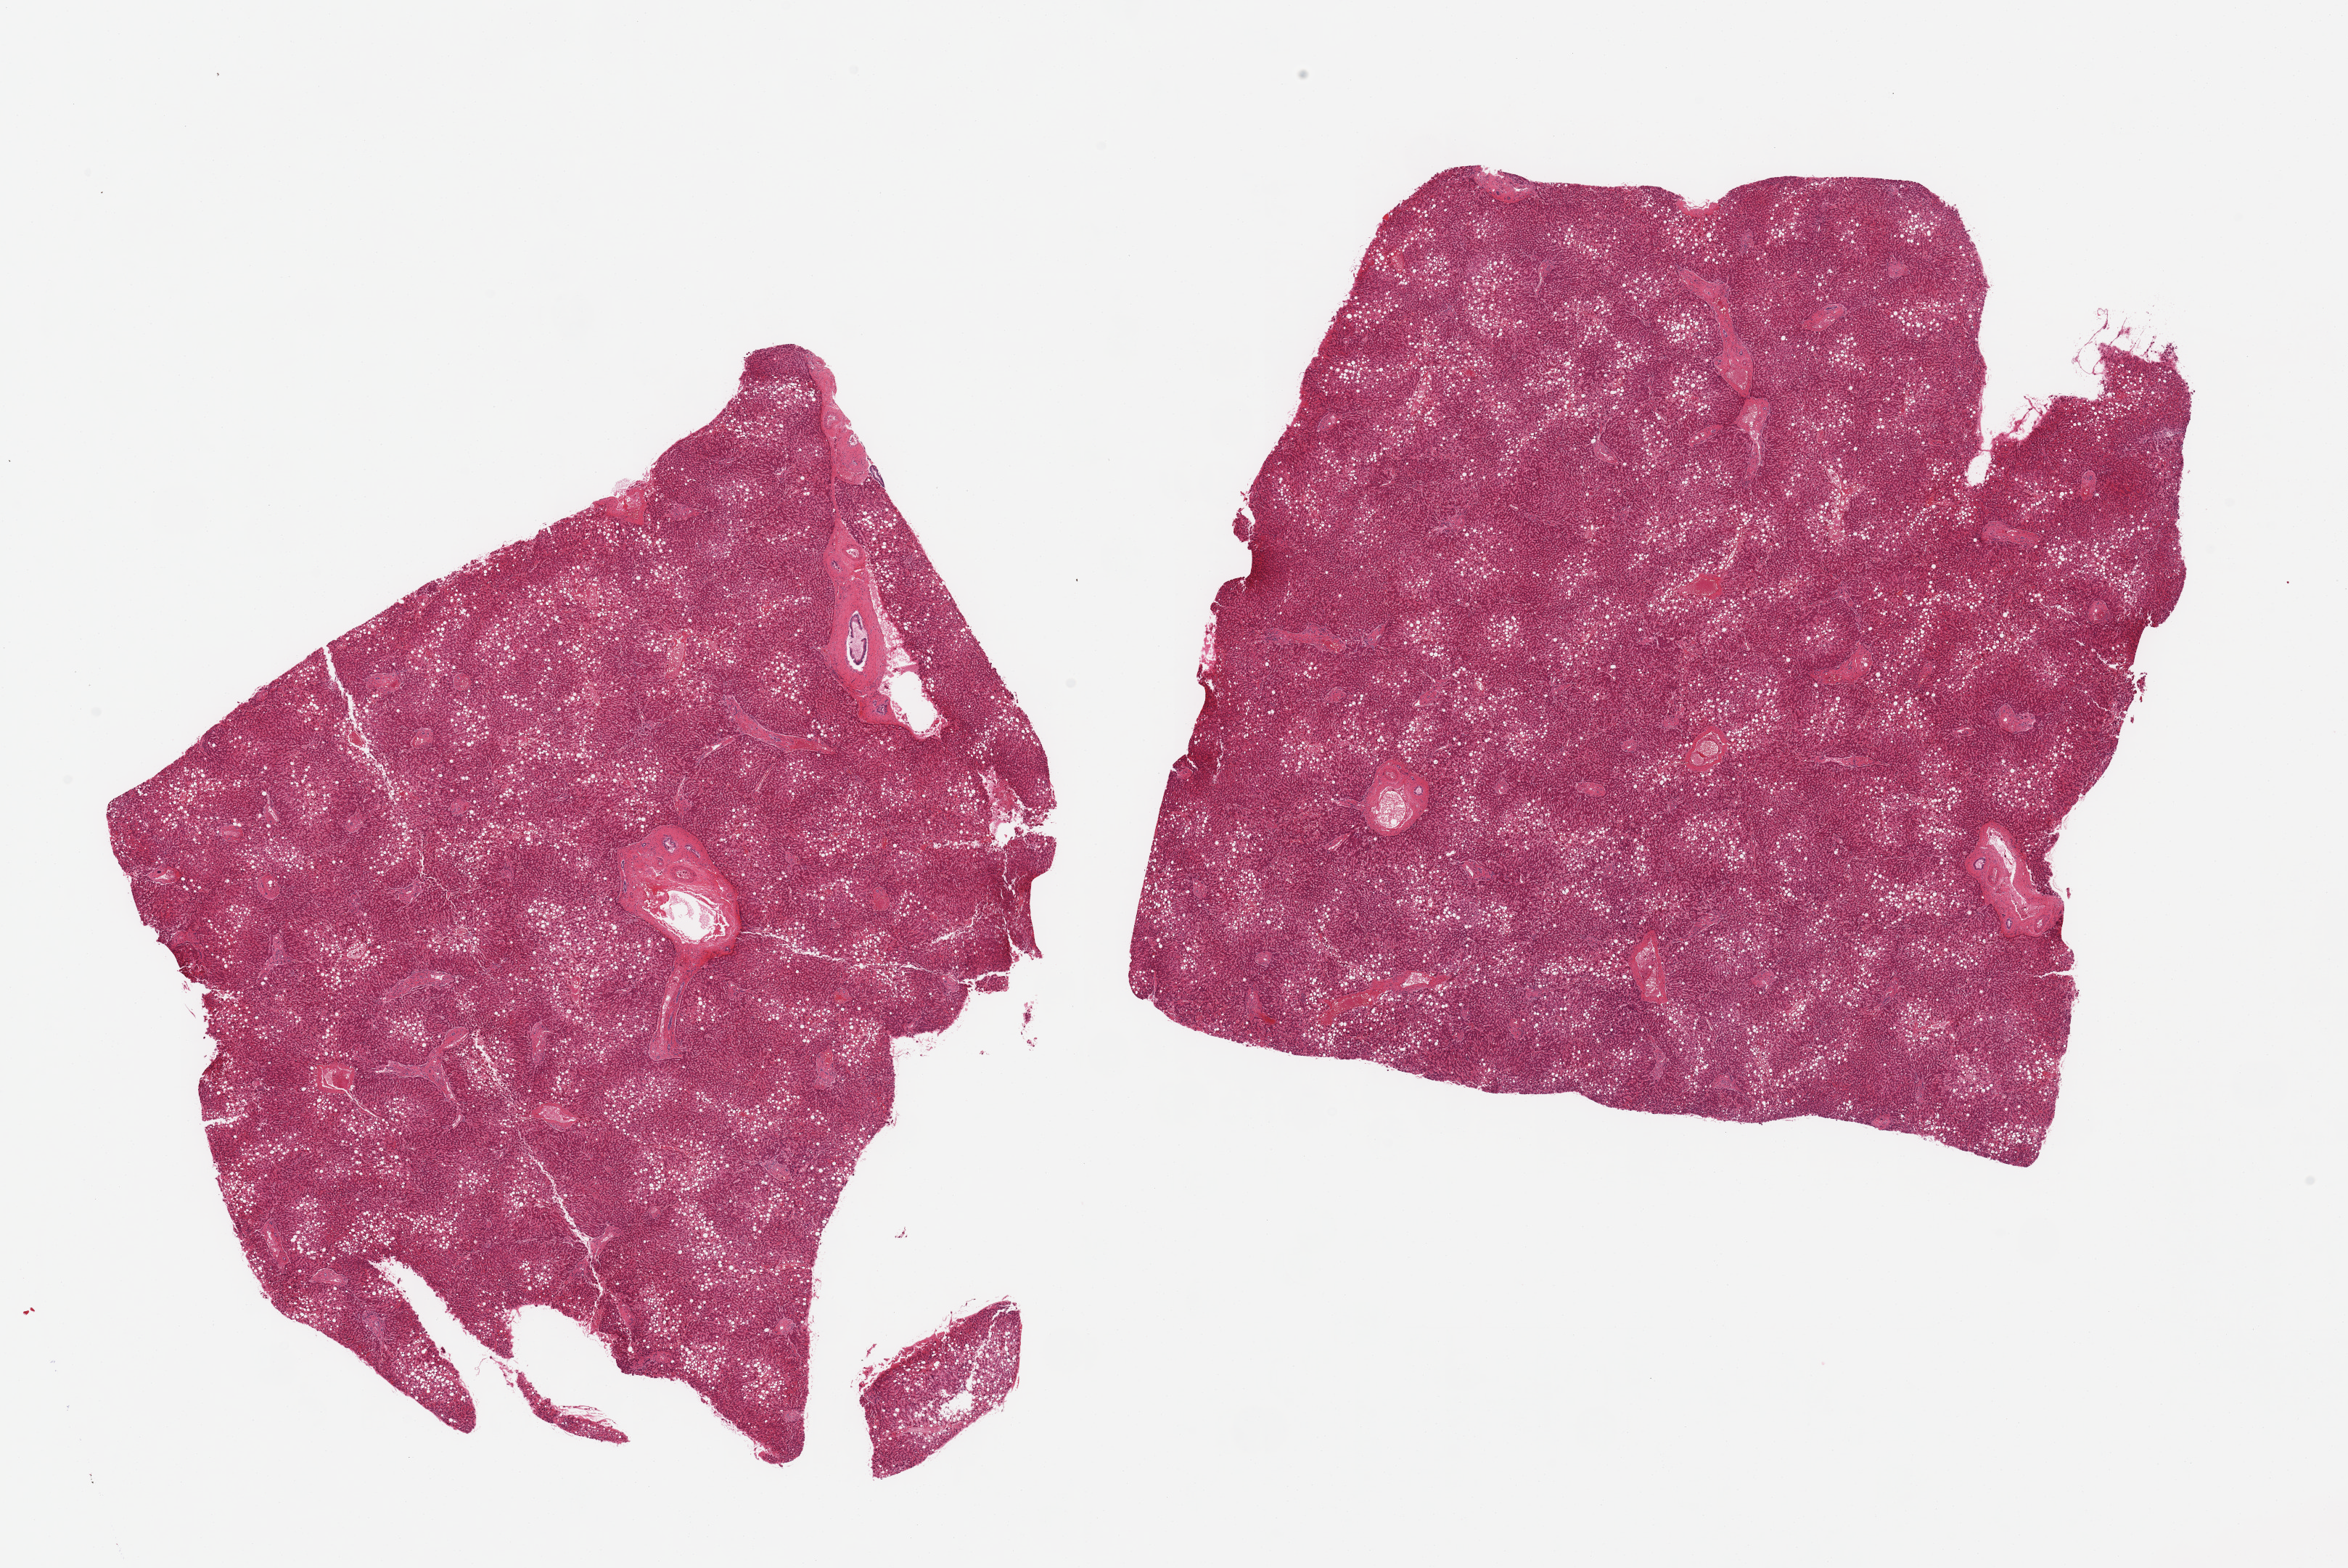
Haematoxylin and eosin whole-slide image — a low-resolution overview of the entire scanned area, about 25.6 x 17.1 mm (acquisition: 20x scan); PAXgene-fixed, paraffin-embedded tissue; target tissue: liver; tissue donor sample. Donor sex: male.
Review note (as recorded): 2 pieces, ~50% macrovesicular steatosis; moderate passive congestion.